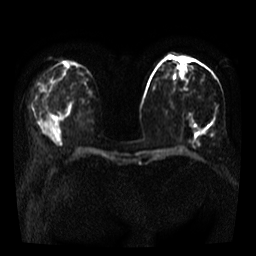
Breast MRI, one axial slice; position 16 of 35 along the scan axis; diffusion-weighted series; image 2 of 4 stored at this slice position (different b-values; order by instance number); 3 T; 256 × 256 image matrix, field of view 320 × 320 mm. Female patient.
Structures marked on this image (manually delineated by an expert):
- tumour on diffusion-weighted imaging: bounding box (x1, y1, x2, y2) in pixels: (196, 129, 205, 134)